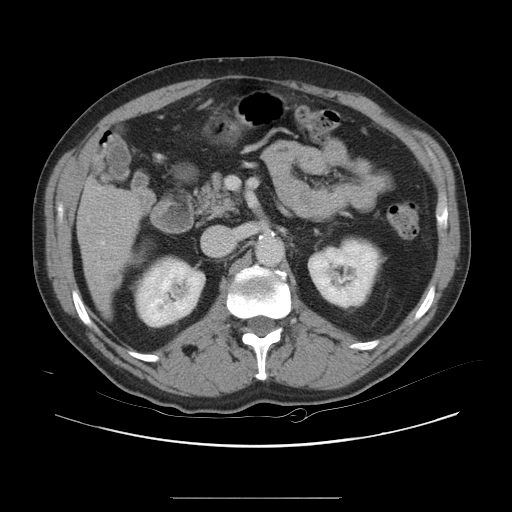
Contrast-enhanced abdominal CT, one axial slice. Slice 9 of 40 in the series (ordered by position). 120 kVp. Soft-tissue window (W 400 / L 40 HU). 512 × 512 image matrix, field of view 408 × 408 mm. Male patient, age 64 years. Case-level facts recorded for this patient, not image findings: diagnosis: colorectal cancer liver metastases, imaged before liver resection; multiple liver metastases: yes; largest metastasis: 3.2 cm; disease in both lobes: yes.
Annotated regions visible in this slice (expert manual segmentation):
- hepatic veins: bounding box [x1, y1, x2, y2] px = [101, 241, 105, 245]
- liver: [78, 181, 141, 310]
- liver metastasis: [105, 269, 120, 284]